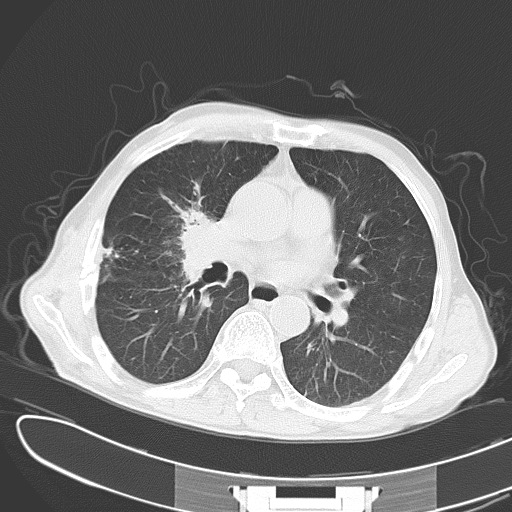
Chest CT, one axial slice; position 18 of 43 along the scan axis; reconstruction kernel B70f; lung window (W 1500 / L -600 HU); 5 mm slice thickness; 512 × 512 image matrix, field of view 353 × 353 mm. Male patient, age 65 years. From the clinical record (not read from this slice): clinical TNM (as recorded): T2 N3 M1; histopathological grade: G3.
Outlined on this slice (rectangle marked by the reading radiologist):
- lung tumour (recorded histology: small cell carcinoma): bounding box <172,199,231,279> (left, top, right, bottom; pixels)